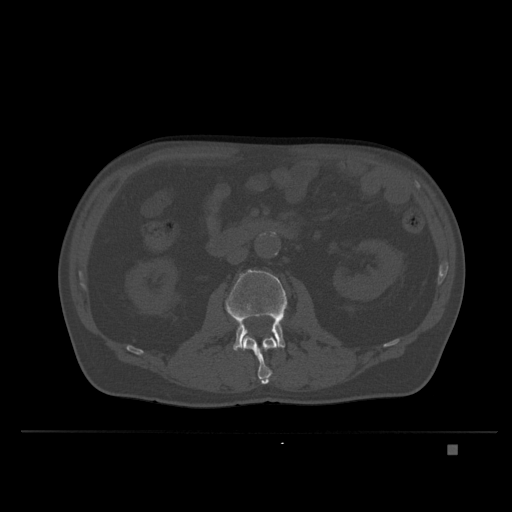
CT including the spine, one axial slice; position 106 of 435 along the scan axis; bone window (W 1800 / L 400 HU); 512 × 512 image matrix, field of view 434 × 434 mm. Patient: male, 73 years. Case-level facts recorded for this patient, not image findings: primary cancer: skin.
Outlined on this slice (semi-automatic segmentation, software-assisted and operator-edited):
- L2 vertebra: bounding box (x1, y1, x2, y2) in pixels: (242, 335, 278, 384)
- L3 vertebra: (225, 270, 288, 351)